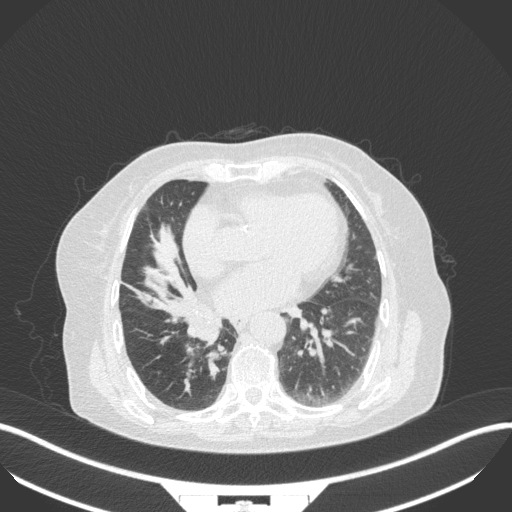
Chest CT, one axial slice. Position 129 of 329 along the scan axis. Lung window (W 1500 / L -600 HU). 1 mm slice thickness. 512 × 512 image matrix. Patient: female, 75 years. From the clinical record (not read from this slice): clinical TNM (as recorded): T1b N0 M1a; histopathological grade: G1.
Structures marked on this image (bounding box drawn by a radiologist):
- lung tumour (recorded histology: squamous cell carcinoma): bounding box (x1, y1, x2, y2) in pixels: (181, 305, 219, 350)